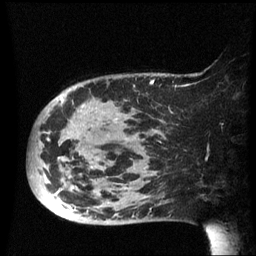
Breast MRI (dynamic contrast-enhanced), one sagittal slice. Dynamic contrast-enhanced series, image 2 of 3 at this slice position (ordered by acquisition). 1.5 T. TE 4.2 ms, TR 8.4 ms. 2.5 mm slice thickness. 256 × 256 image matrix, field of view 220 × 220 mm. Patient: female, 49 years.
Outlined on this slice (semi-automatically segmented with operator editing):
- analysis volume of interest (the breast-tissue region the enhancement analysis was run in; not a lesion): bounding box [x1, y1, x2, y2] px = [29, 74, 182, 225]
- tumour enhancement mask (voxels above the 70 % enhancement threshold inside the analysis volume of interest): [49, 80, 155, 189]